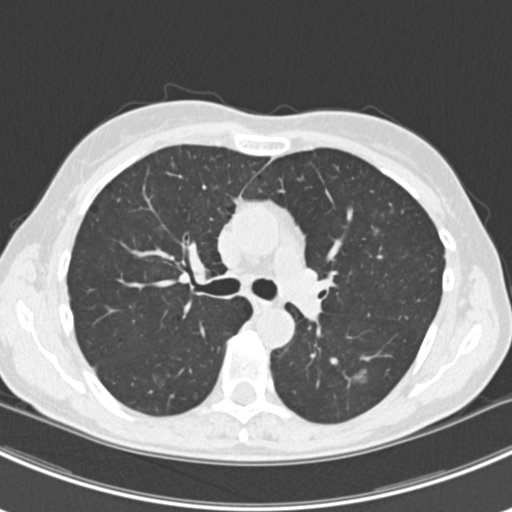
Chest CT (low-dose screening protocol), one axial image, first (baseline) screen, lung window (W 1500 / L -600 HU), 2 mm slice thickness, 120 kVp, slice 69 of 224 in the series, 512 × 512 image matrix. Female, age 63 years at enrolment. Current smoker at enrolment.
2 lesions marked by an expert reader on this slice (largest first), box from (x=134, y=362) to (x=180, y=403) px; (x=343, y=362)–(x=381, y=393). The screening reader recorded 10 non-calcified nodules or masses ≥4 mm on this exam (right lower lobe, right lower lobe, left lower lobe, left lower lobe, right middle lobe, right lower lobe, left lower lobe, left upper lobe, right upper lobe, left upper lobe); which of them these boxes mark is not recorded. Lung cancer was diagnosed 751 days after this screen: bronchiolo-alveolar adenocarcinoma, NOS, right upper lobe, right middle lobe, right lower lobe, left upper lobe, left lower lobe, moderately differentiated (G2), stage IV (AJCC 6th edition).